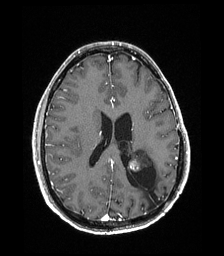
Brain MRI from a brain-tumour surgery series, one axial slice. Slice 80 of 192 in the series (ordered by position). T1-weighted post-contrast. 224 × 256 image matrix, field of view 224 × 256 mm. Case-level facts recorded for this patient, not image findings: histopathology: Low grade glioma; IDH mutation: no; tumour location: Left Parieto-Occipital Intraventricular.
Structures marked on this image (manually delineated by an expert):
- previous resection cavity: bounding box [x1, y1, x2, y2] px = [127, 166, 162, 208]
- tumour: [128, 148, 152, 172]